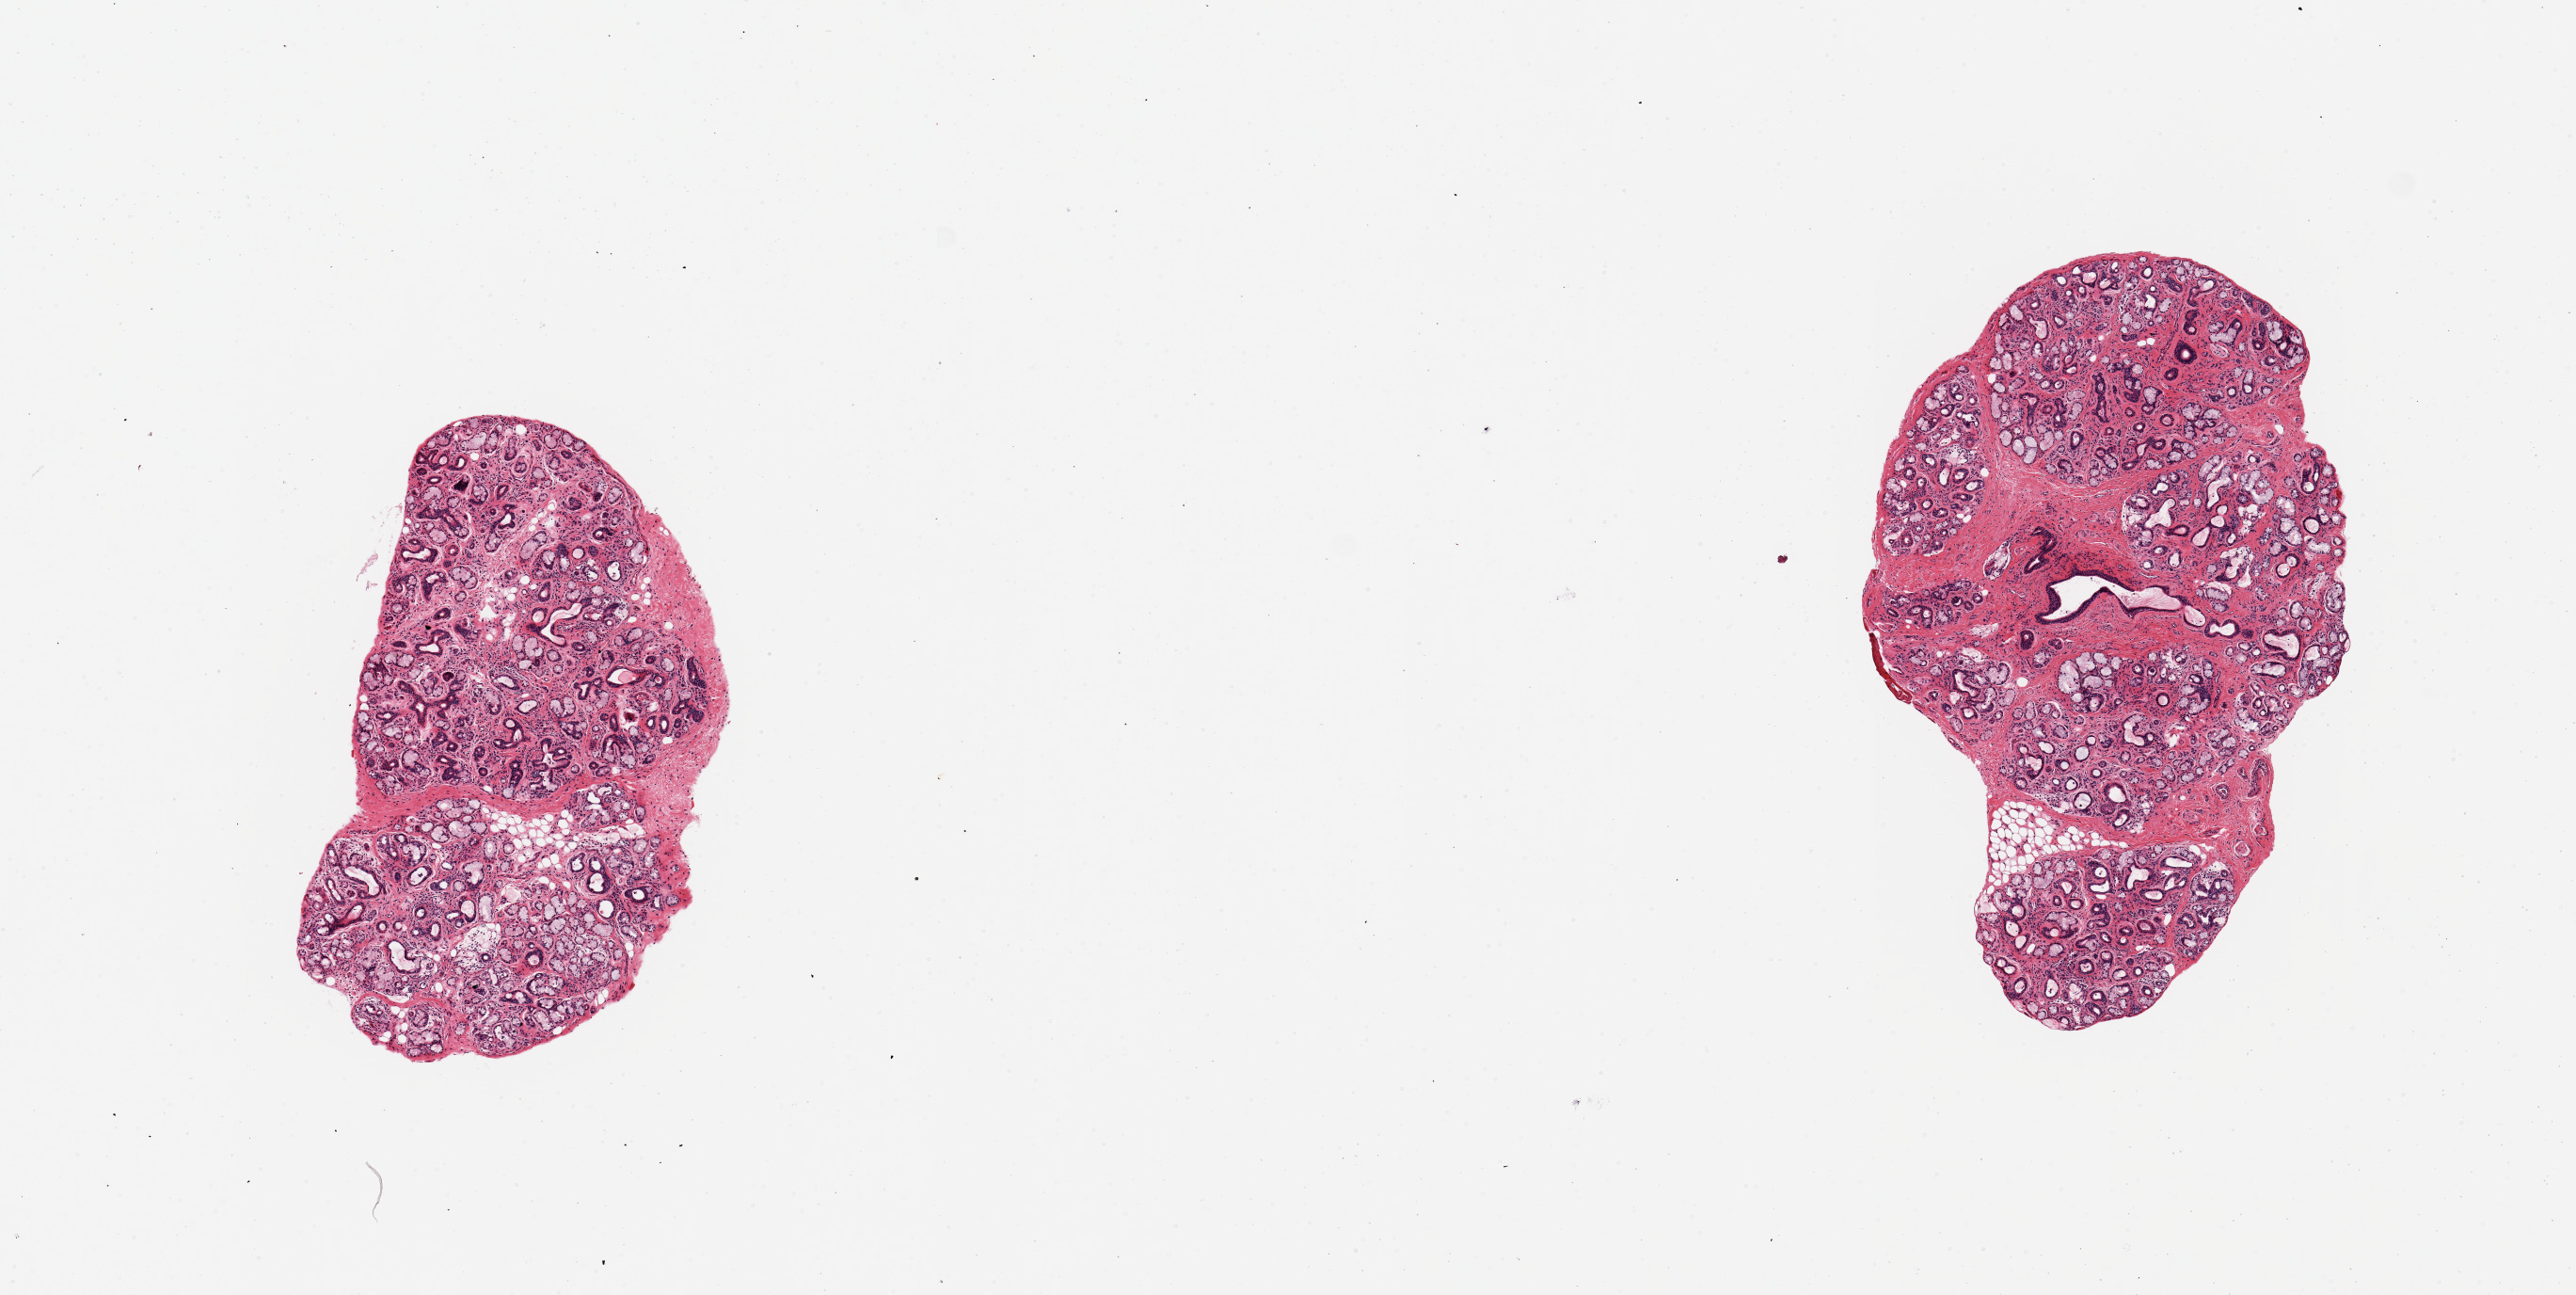
Digitized hematoxylin and eosin (H&E)-stained section, shown as a low-resolution overview of the whole scanned area (about 10.8 x 5.4 mm). PAXgene-fixed paraffin-embedded (PFPE) section. Target tissue: minor salivary gland. Tissue donor sample. Male donor.
Reviewer comment on this tissue sample: 2 pieces; well dissected glands with moderate atrophy and fibrosis; less than 5% of internal fat.